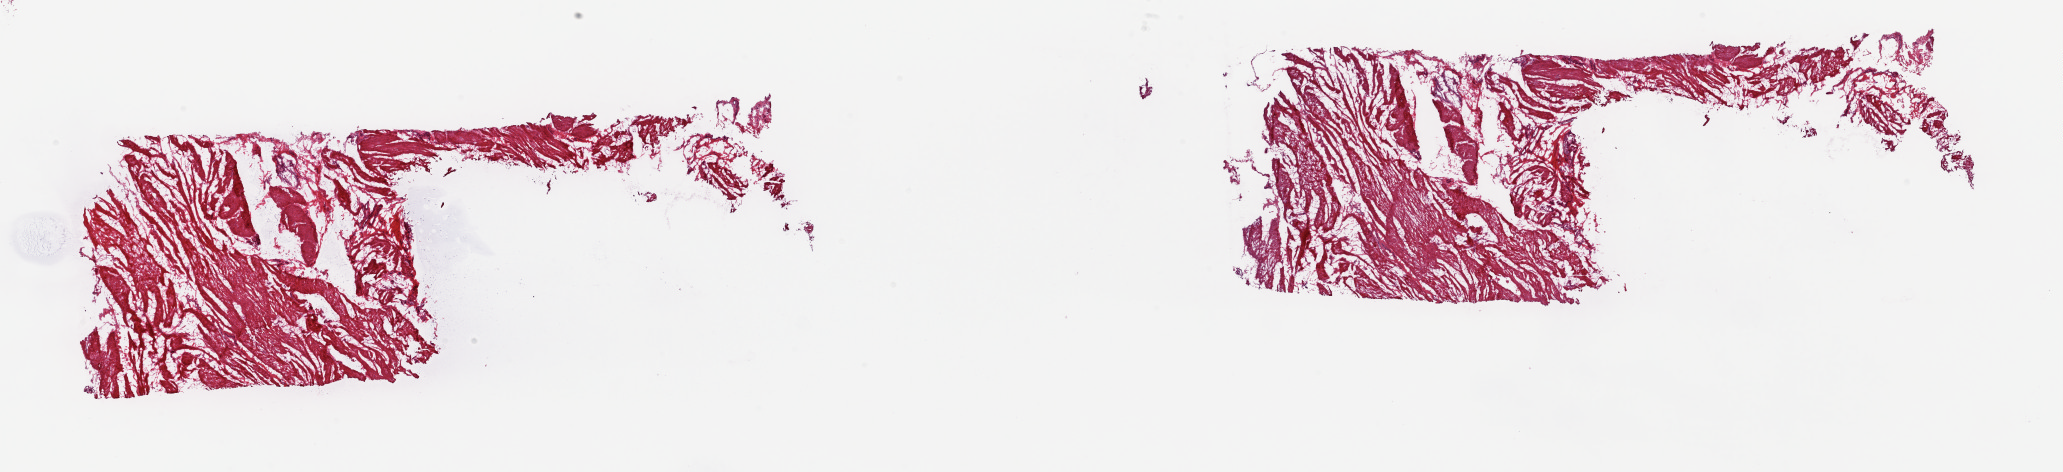
H&E whole-slide image, a low-resolution overview of the entire scanned area, about 32.7 x 7.5 mm (from a 20x scan); frozen section from the top of the tissue portion; sample: solid tissue normal (non-tumour tissue), connective, subcutaneous and other soft tissues. Patient: male, age at initial diagnosis 42 years. Composition of this section per pathologist review: tumour cells 0%, tumour nuclei 0%, normal cells 100%, stromal cells 0%, necrosis 0%. Inflammatory infiltration, as recorded: lymphocyte infiltration 0%, monocyte infiltration 0%, neutrophil infiltration 0%.
* this section: solid tissue normal sample (biorepository sample class)
* patient diagnosis: Leiomyosarcoma, NOS (connective, subcutaneous and other soft tissues of pelvis)